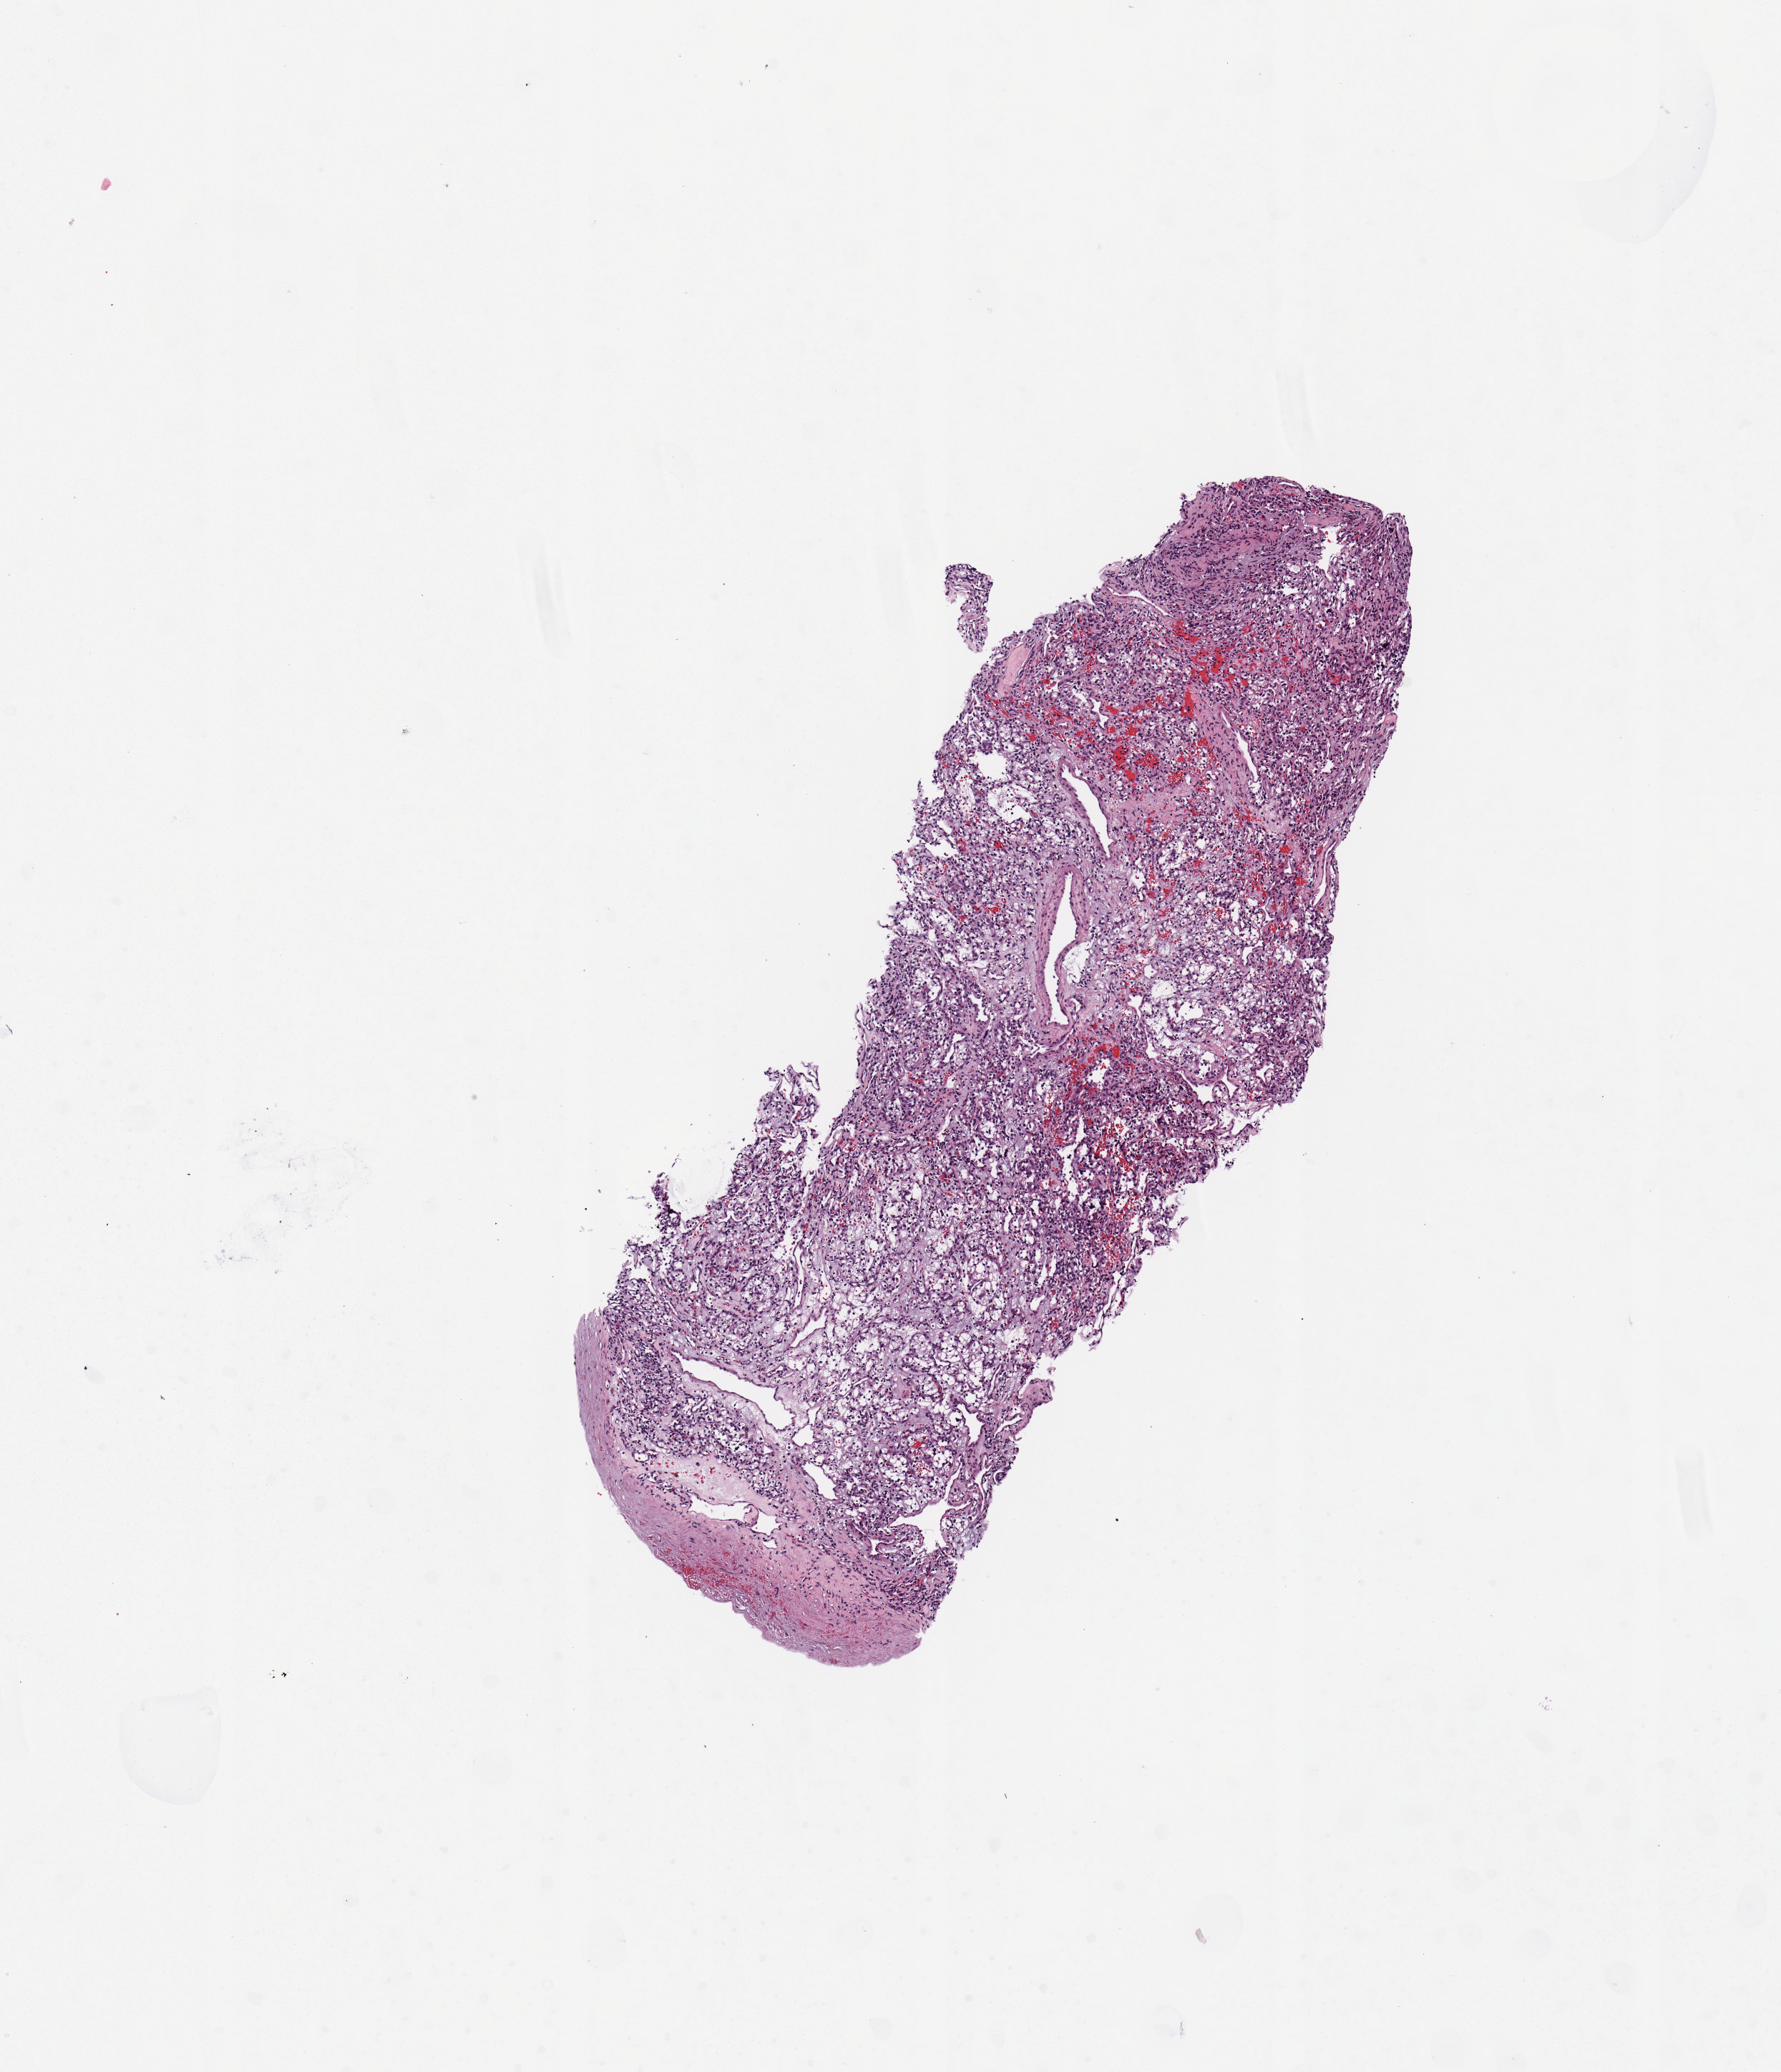
Whole-slide histology image, H&E, whole scanned area (about 4.9 x 5.7 mm, acquisition: 20x scan) shown as a low-resolution overview; tumour tissue sample, sampled site: kidney. Patient: female, age 33 years.
Histologic diagnosis: Renal cell carcinoma, NOS.